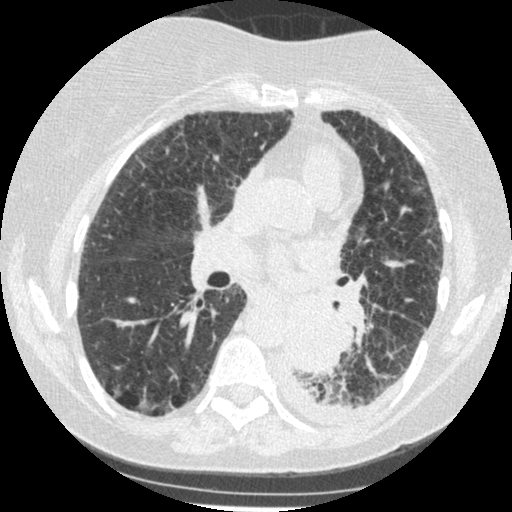
Axial slice from a low-dose chest CT screening exam, third annual screen, lung window (W 1500 / L -600 HU), 1.25 mm slice thickness, slice 211 of 341 in the series. Female, age 60 years at enrolment.
• Expert reader's lesion annotation, box from (x=272, y=306) to (x=342, y=375) px.
• Screening reader's record for this exam (one nodule recorded; not confirmed to be the boxed lesion): non-calcified nodule or mass ≥4 mm, left lower lobe, 54 × 38 mm, smooth margins, soft tissue attenuation, pre-existing on the prior screen: yes; interval growth: yes.
• Official screen result: positive, other.
• Later outcome: lung cancer diagnosed 15 days after this screen — small cell carcinoma, NOS, left lower lobe, undifferentiated (G4), stage IV (AJCC 6th edition), 69 mm at pathology.